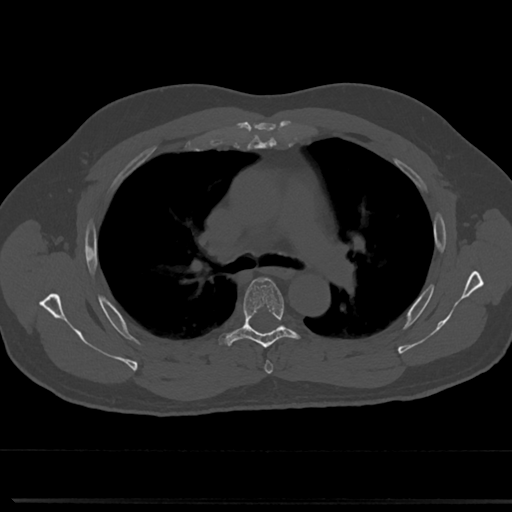
CT including the spine, one axial slice. Position 503 of 817 along the scan axis. Reconstruction kernel Br40s/3. 120 kVp. Bone window (W 1800 / L 400 HU). 512 × 512 image matrix, field of view 355 × 355 mm. Male patient, age 61 years. From the clinical record (not read from this slice): primary cancer: prostate.
Annotated regions visible in this slice (semi-automatic segmentation, software-assisted and operator-edited):
- T4 vertebra: box from (x=264, y=350) to (x=273, y=374) px
- T5 vertebra: (x=218, y=276)–(x=309, y=352)